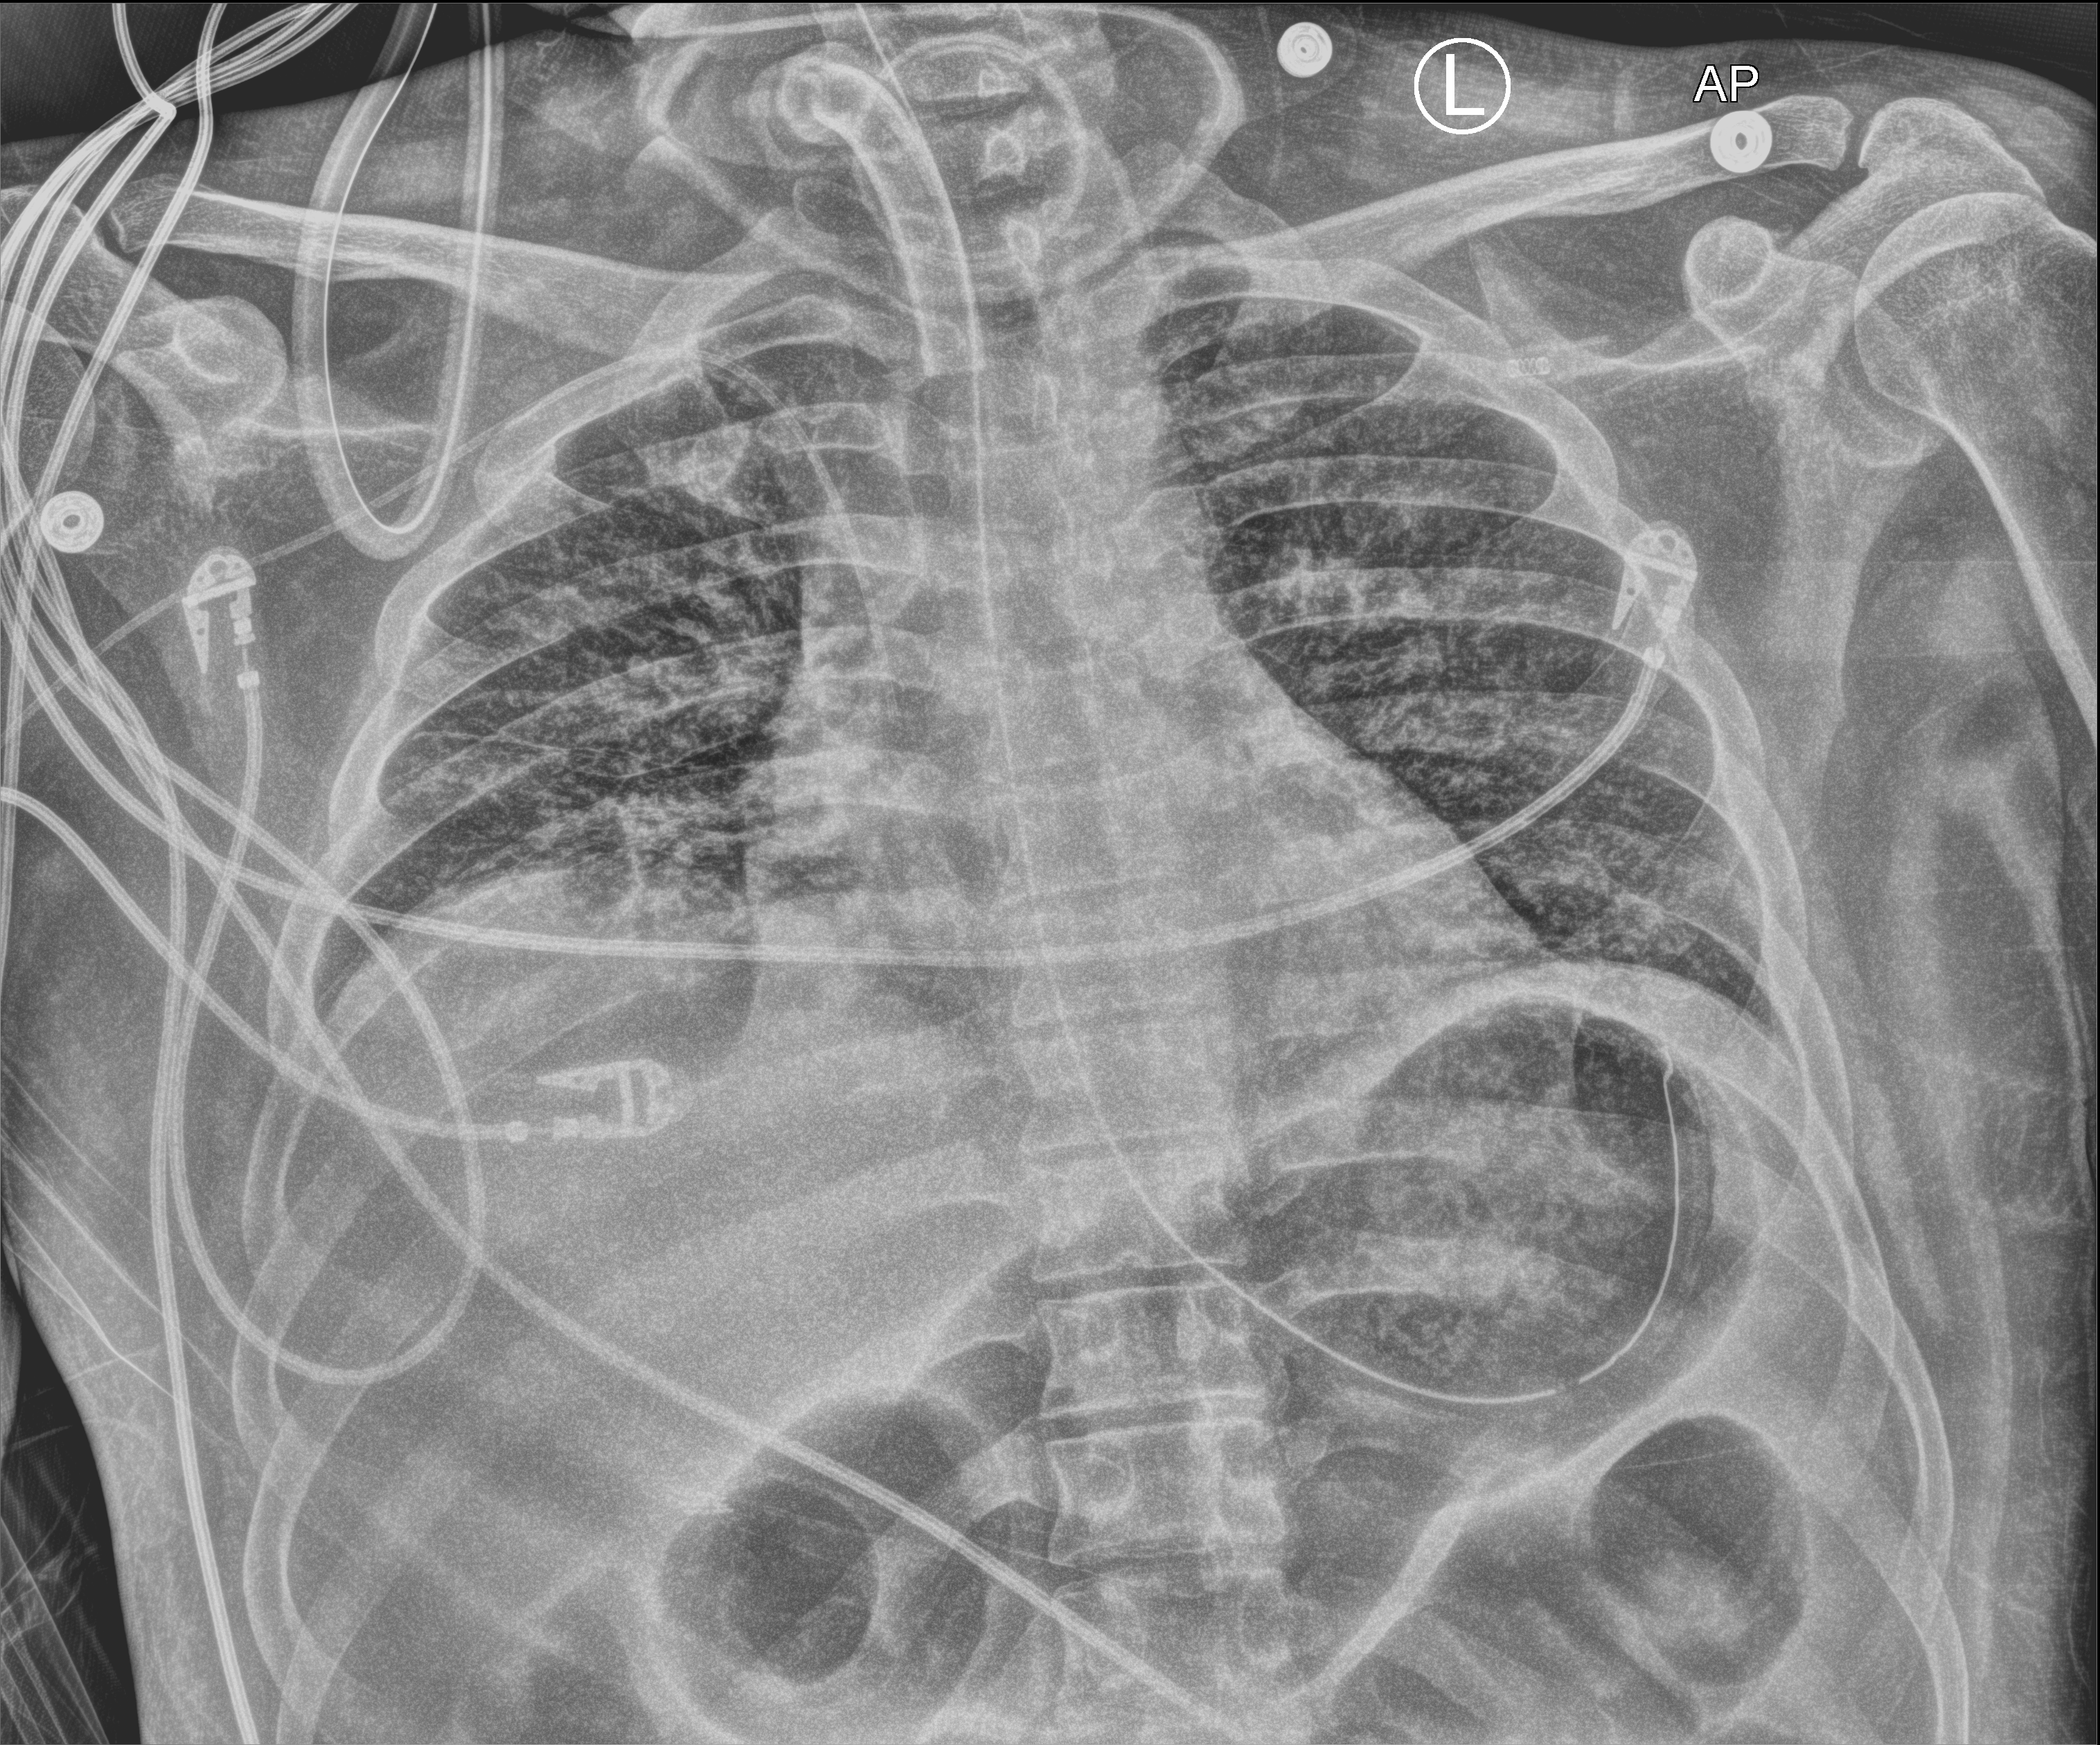
Chest X-ray (portable), anteroposterior (AP) projection. Patient hospitalised with COVID-19; male, aged 18–59 years.
Hospital-stay facts (about this admission, not read from this image; timing relative to this image not recorded): length of hospital stay: 44 days; hypertension (admission record): no.